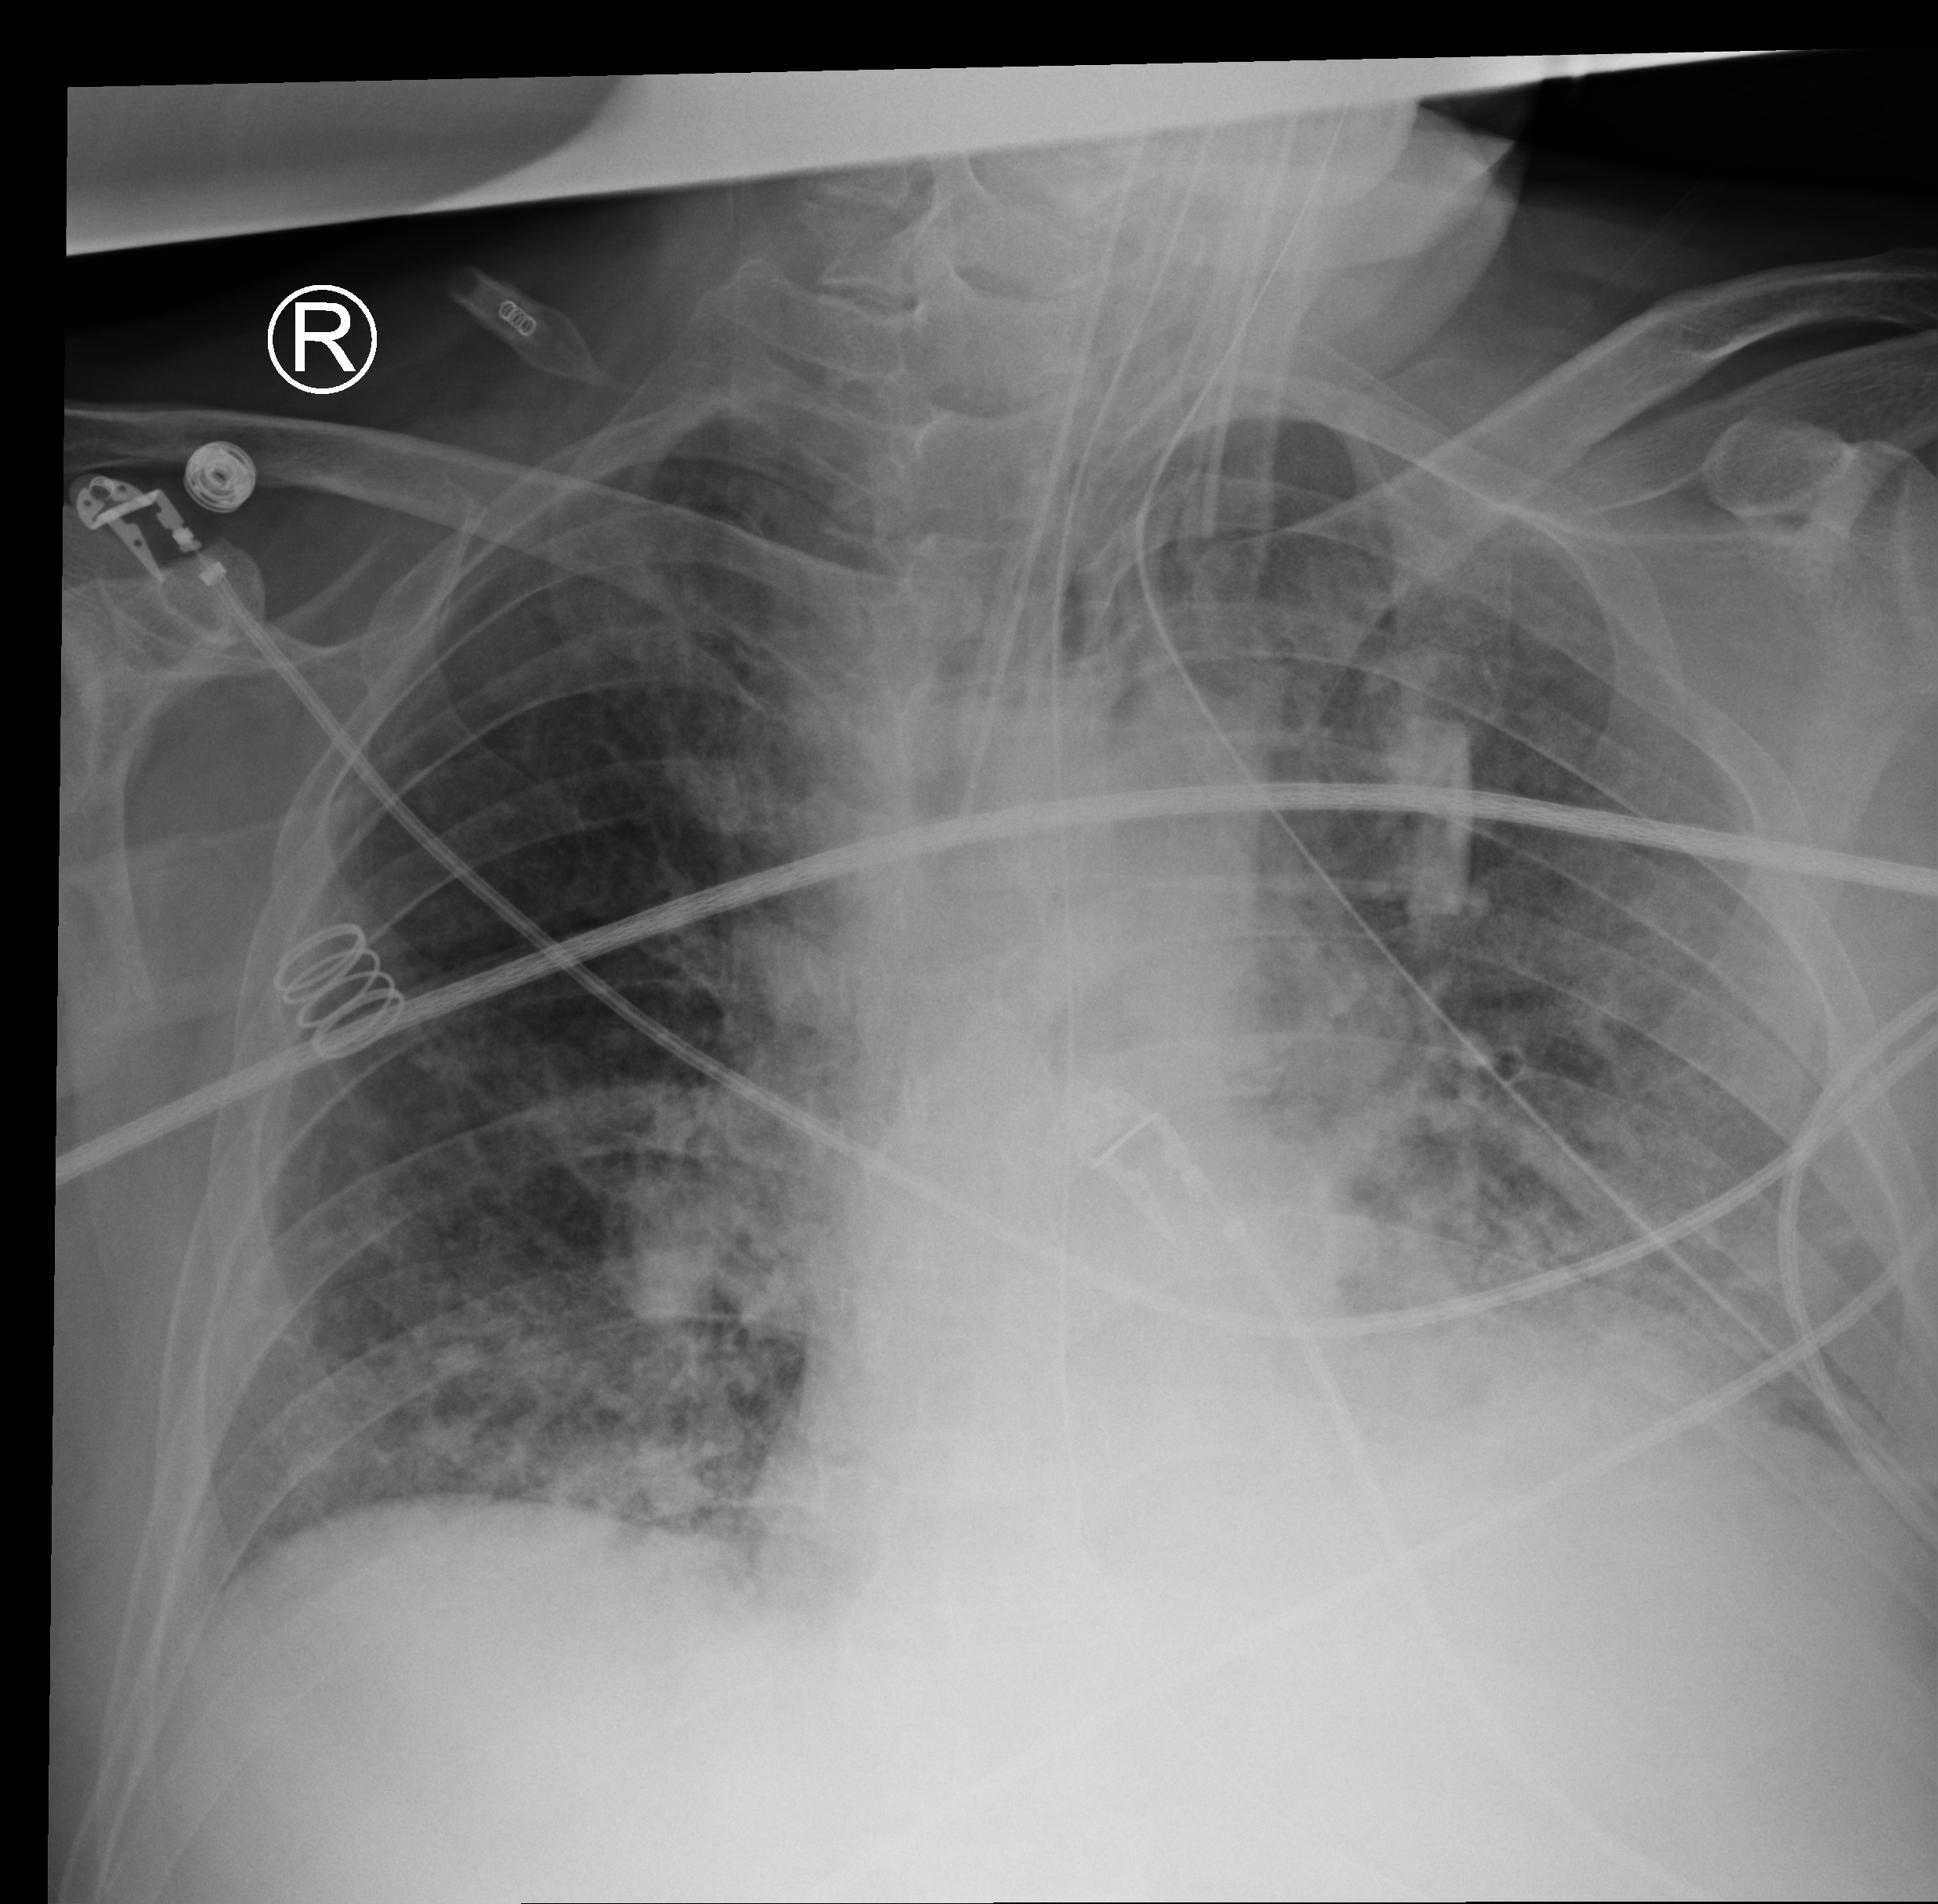
Bedside chest radiograph (computed radiography). Male patient hospitalised with COVID-19, age 18–59 years.
Admission-level facts for this patient (not findings on this image; timing relative to this image not recorded):
- admitted to intensive care during this hospital stay: no